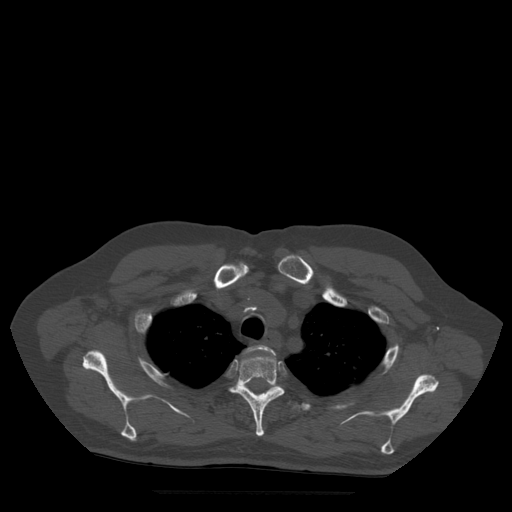
CT including the spine, one axial slice. Slice 408 of 522 in the series (ordered by position). Bone window (W 1800 / L 400 HU). 1.25 mm slice thickness. 512 × 512 image matrix, field of view 420 × 420 mm. Patient age 72 years. From the clinical record (not read from this slice): primary cancer: prostate.
Annotated regions visible in this slice (semi-automatic segmentation, software-assisted and operator-edited):
- T2 vertebra: bounding box <247,345,276,358> (left, top, right, bottom; pixels)
- T3 vertebra: <230,355,285,437>
- T4 vertebra: <242,384,302,410>